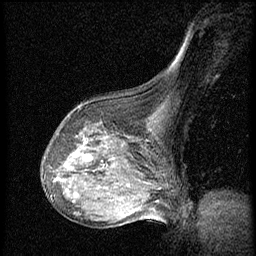
Breast MRI (dynamic contrast-enhanced), one sagittal slice. Position 40 of 56 along the scan axis. Dynamic contrast-enhanced series, image 2 of 3 at this slice position (ordered by acquisition). 1.5 T. TE 4.2 ms, TR 20.4 ms. 256 × 256 image matrix. Female patient, age 64 years. From the clinical record (not read from this slice): setting: breast cancer imaged before/during neoadjuvant chemotherapy; receptor status: HR-positive, HER2-negative.
Structures marked on this image (semi-automatic segmentation, software-assisted and operator-edited):
- analysis volume of interest (the breast-tissue region the enhancement analysis was run in; not a lesion): box from (x=48, y=101) to (x=142, y=186) px
- tumour enhancement mask (voxels above the 70 % enhancement threshold inside the analysis volume of interest): (x=73, y=153)–(x=76, y=156)